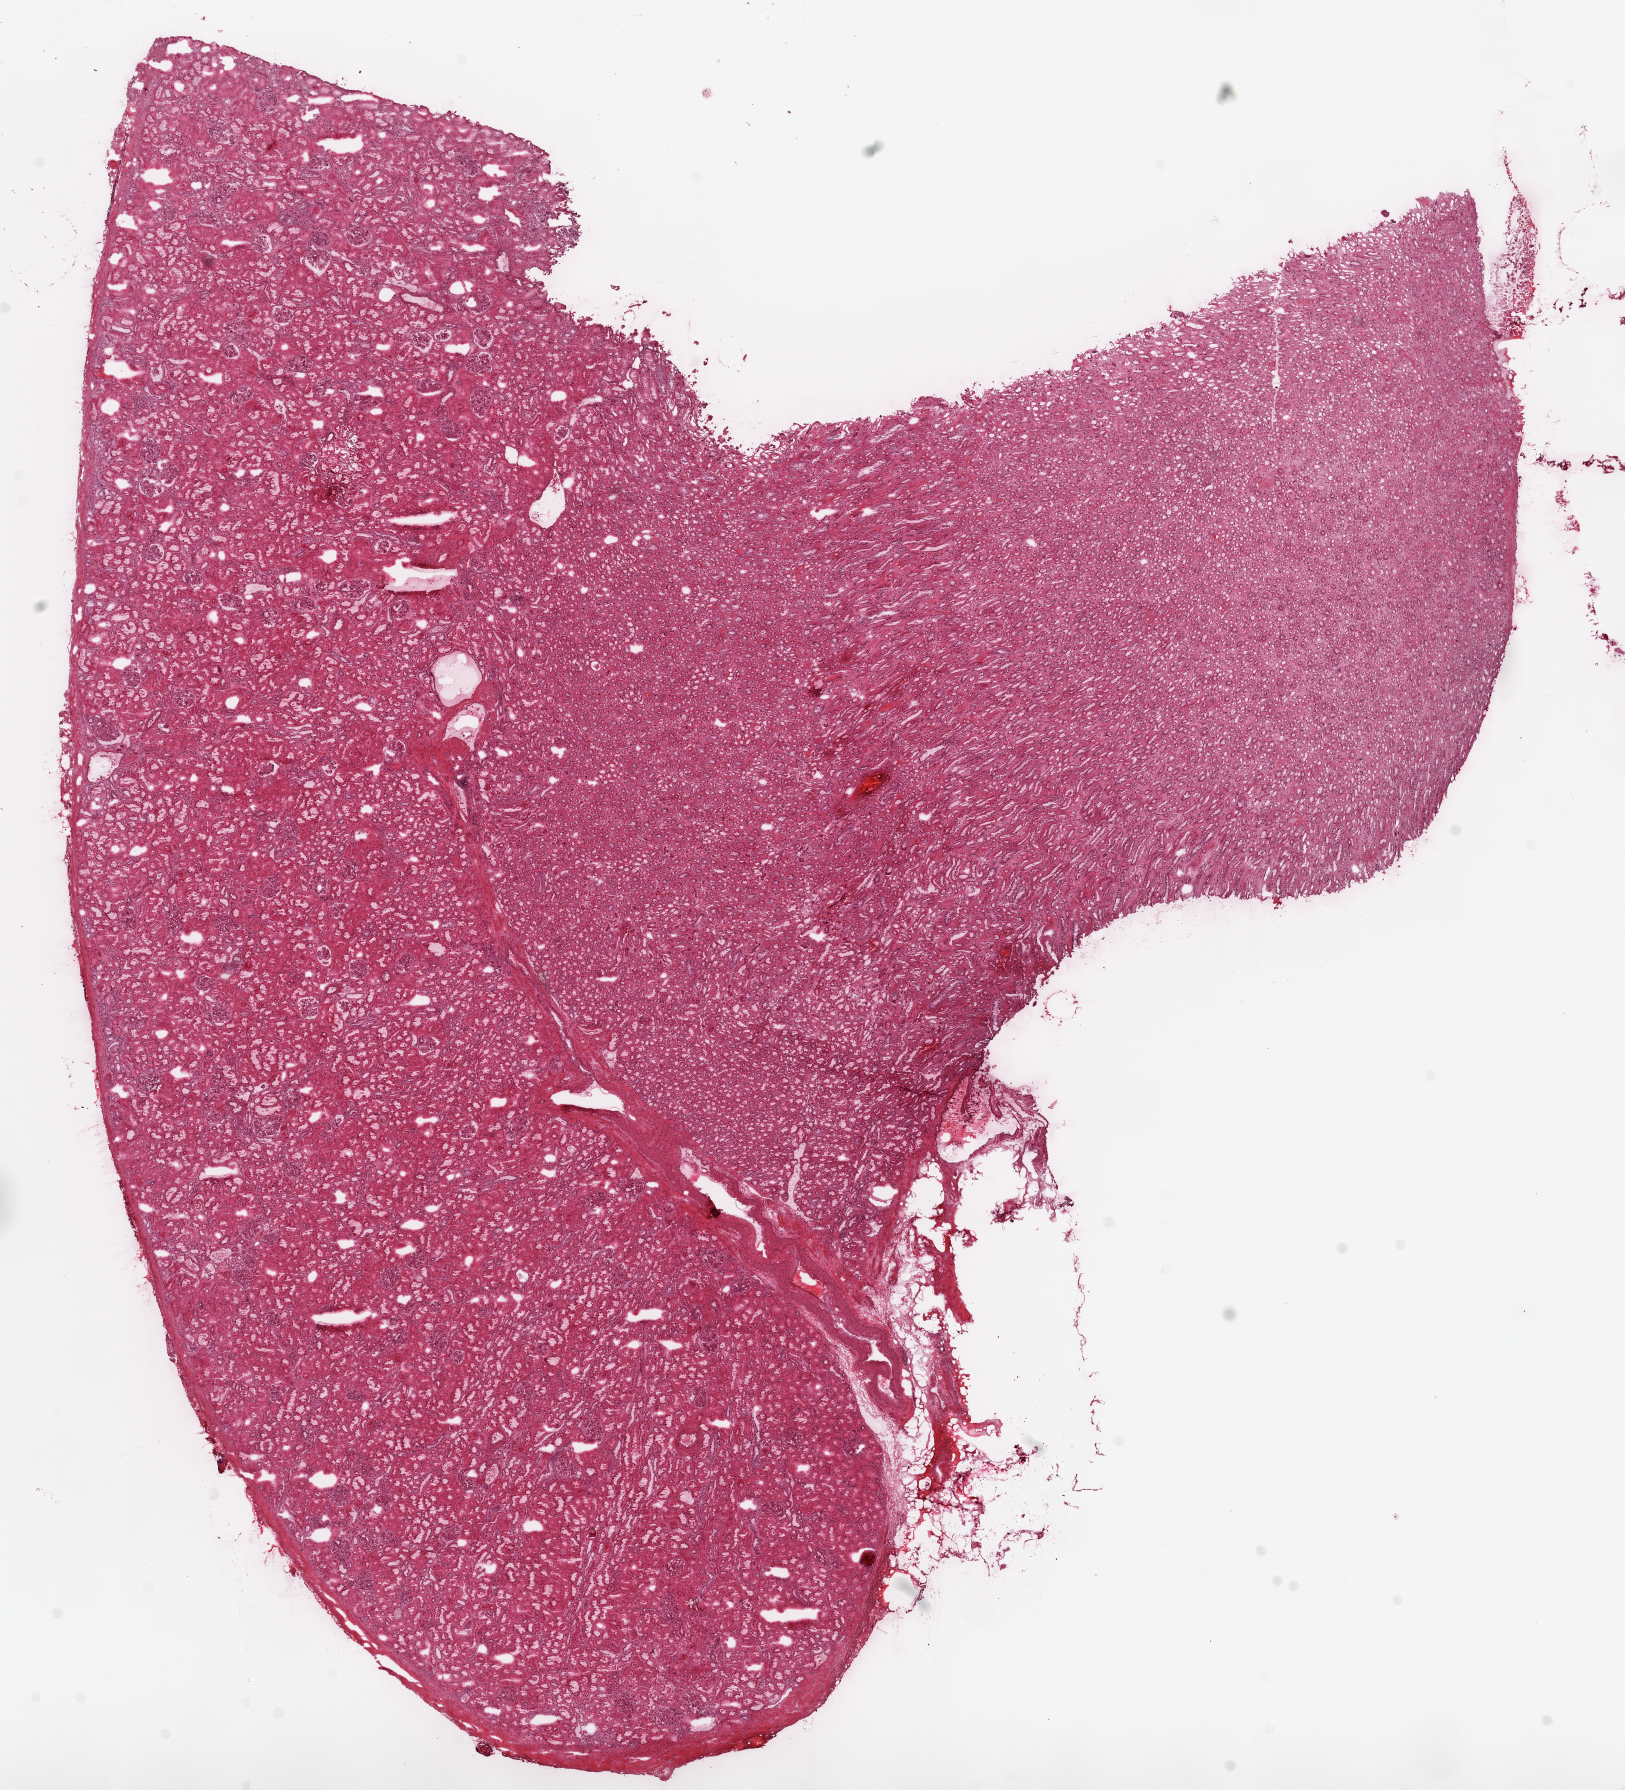
Digitized H&E-stained tissue section (whole slide), whole scanned area (about 13.0 x 14.4 mm, slide scanned at 20x) shown as a low-resolution overview; frozen section; kidney, solid tissue normal (non-tumour tissue) sample. Patient: female, age at initial diagnosis 64 years.
- this section: solid tissue normal sample (biorepository sample class)
- patient diagnosis: Clear cell adenocarcinoma, NOS